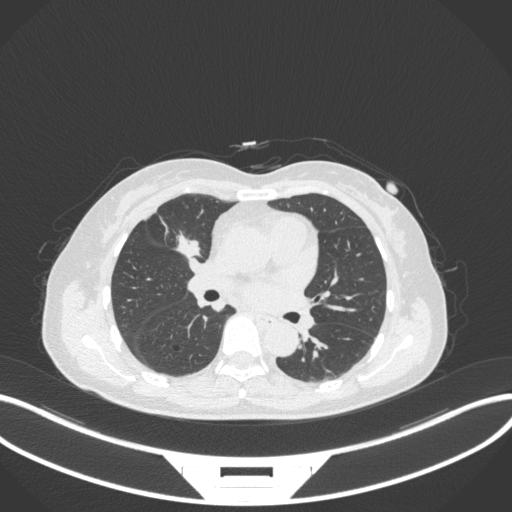
Chest CT, one axial slice; slice 162 of 282 in the series (ordered by position); lung window (W 1500 / L -600 HU); 1 mm slice thickness; 512 × 512 image matrix, field of view 400 × 400 mm. Patient: female, 51 years. From the clinical record (not read from this slice): clinical TNM (as recorded): T1c N0 M0; histopathological grade: G2.
Structures marked on this image (bounding box drawn by a radiologist):
- lung tumour (recorded histology: adenocarcinoma): bounding box (x1, y1, x2, y2) in pixels: (168, 224, 204, 262)